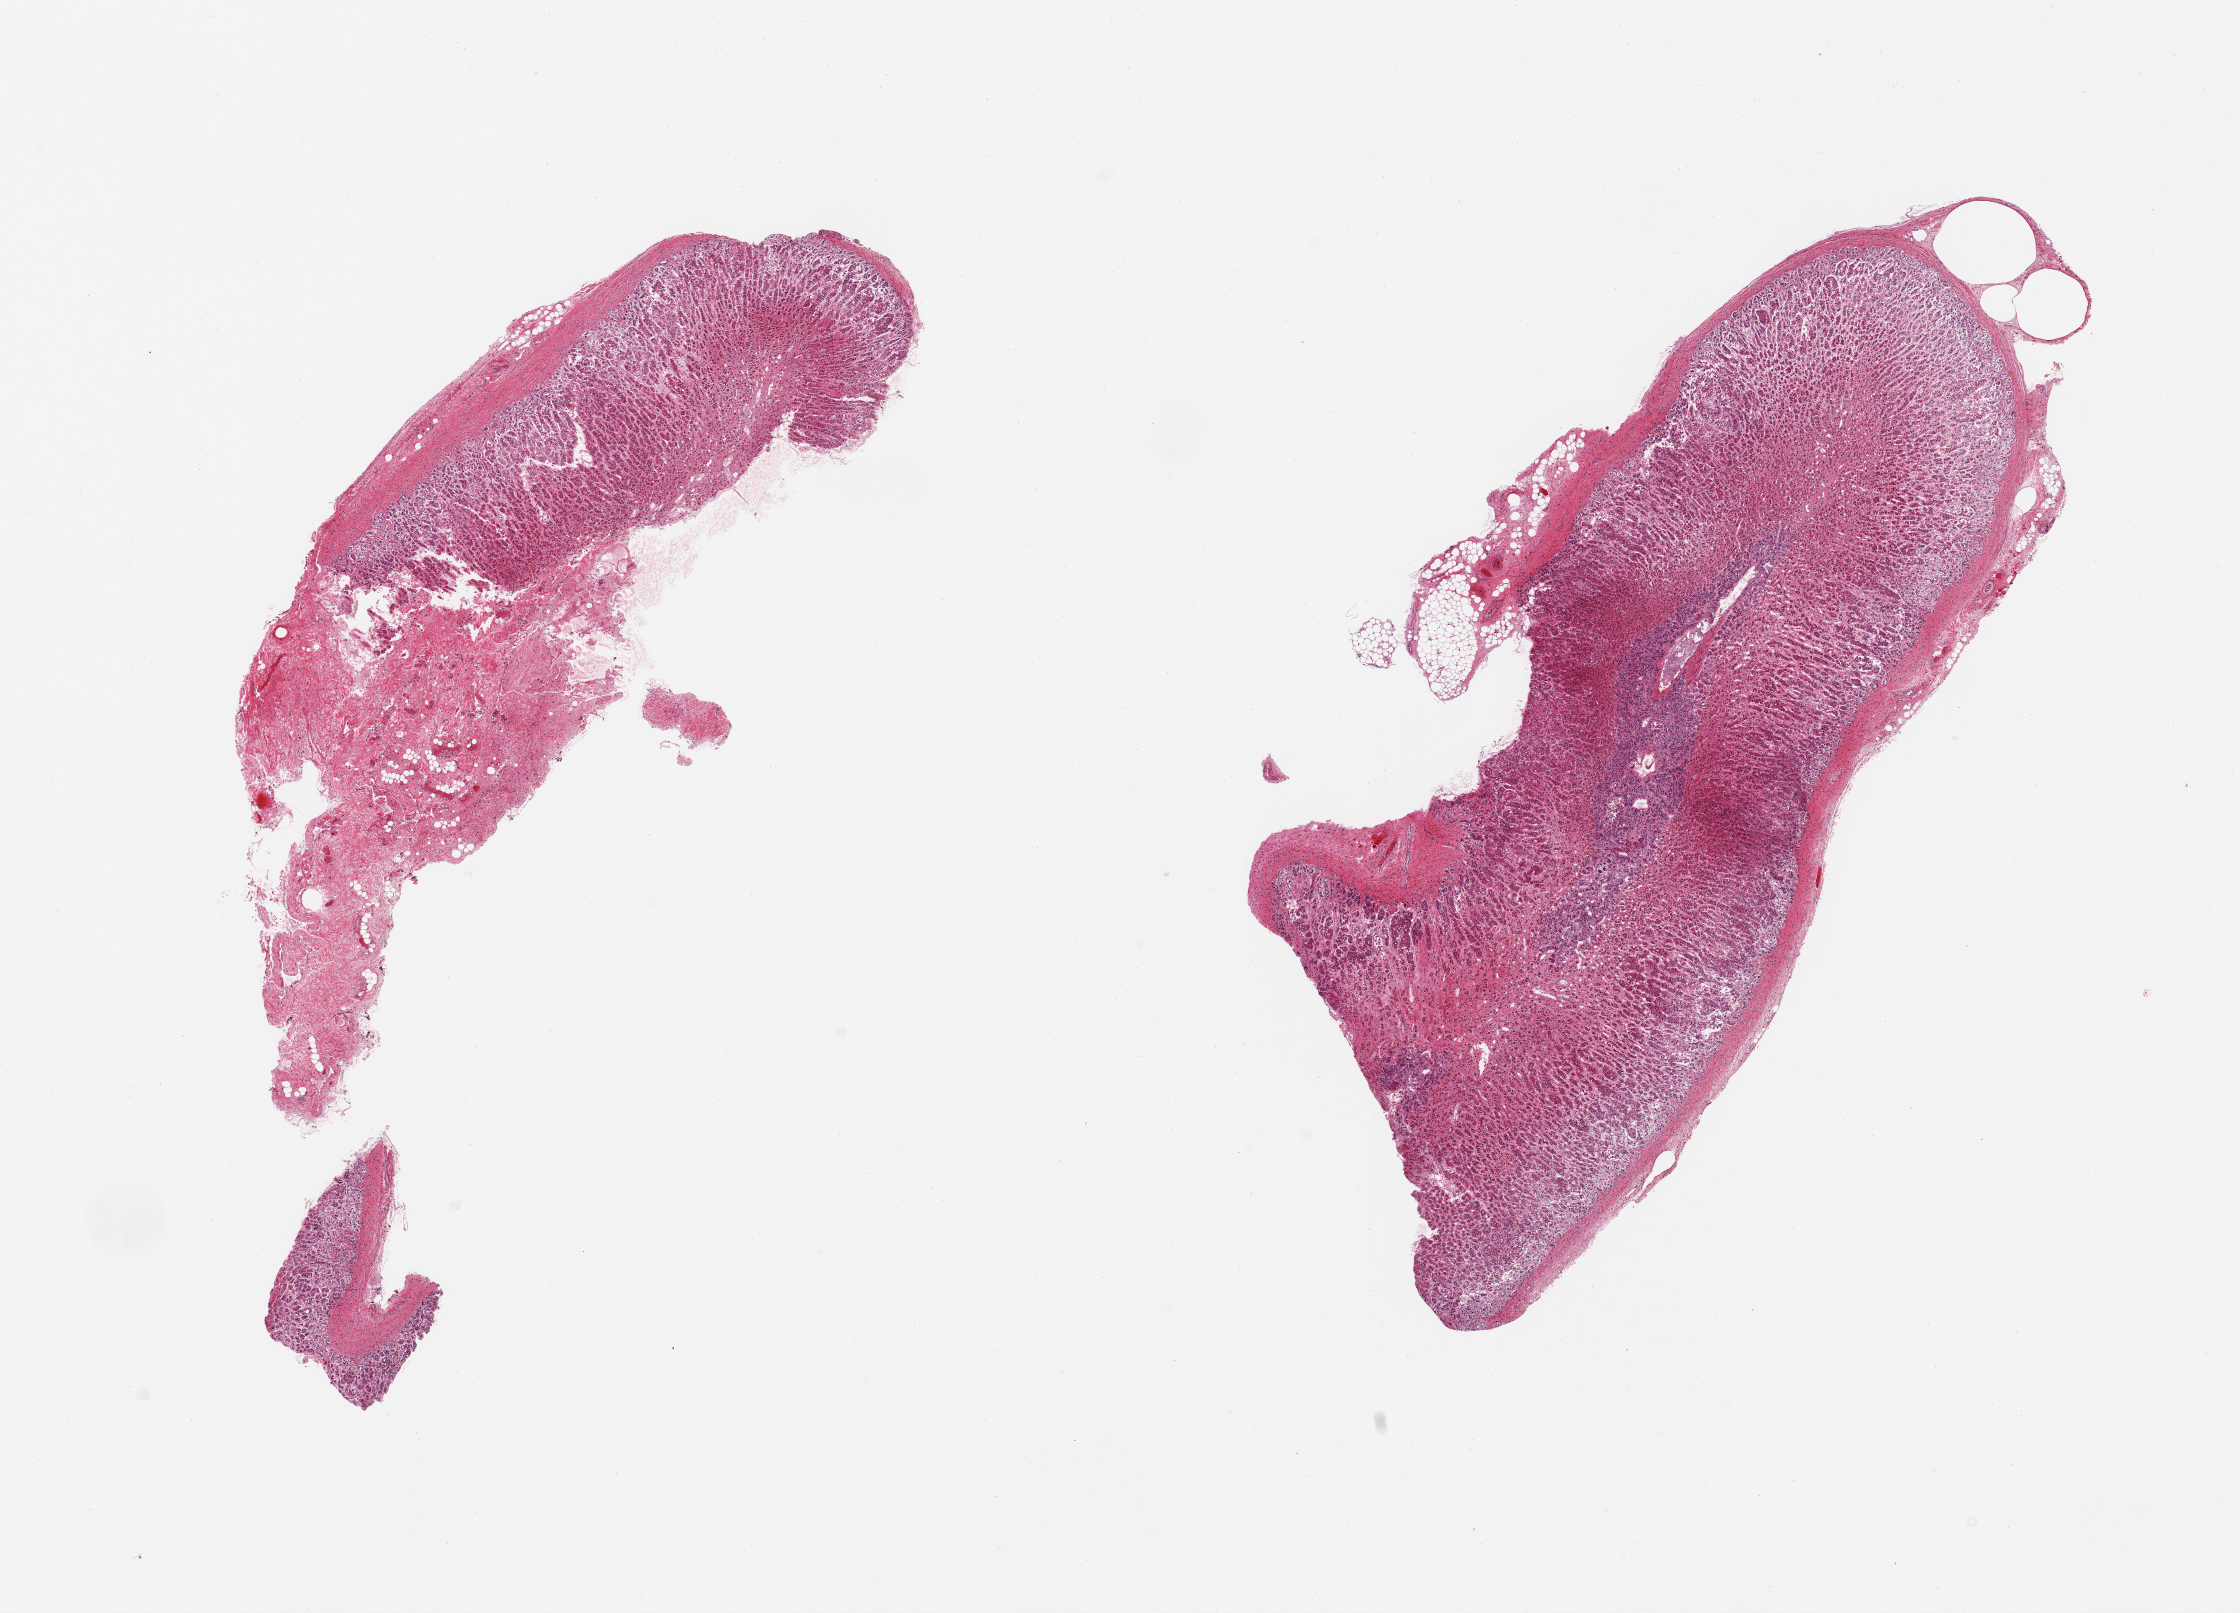
Digitized H&E-stained section, low-resolution overview of the scanned area, about 17.7 x 12.8 mm. PAXgene-fixed, paraffin-embedded tissue. Target tissue: adrenal gland. Donor tissue sample. Female donor.
Reviewer comment on this tissue sample: 2 pieces, mainly cortex, focal medulla but moderate-advanced autolysis.